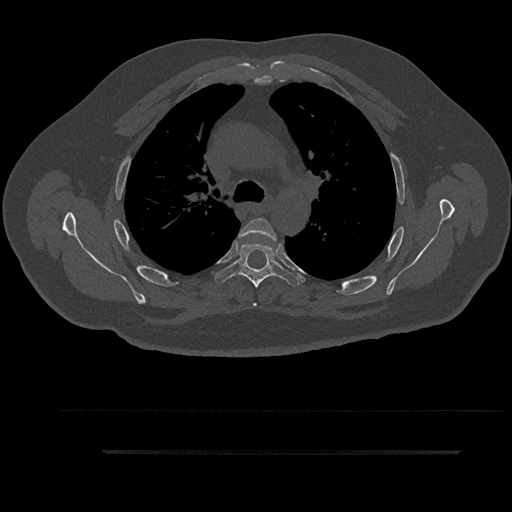
CT including the spine, one axial slice; reconstruction kernel Br40s/3; 120 kVp; bone window (W 1800 / L 400 HU); 0.5 mm slice thickness; 512 × 512 image matrix, field of view 432 × 432 mm. Patient: male, 63 years. From the clinical record (not read from this slice): primary cancer: renal.
Annotated regions visible in this slice (semi-automatic segmentation, software-assisted and operator-edited):
- T4 vertebra: box from (x=238, y=218) to (x=278, y=306) px
- T5 vertebra: (x=215, y=243)–(x=299, y=289)